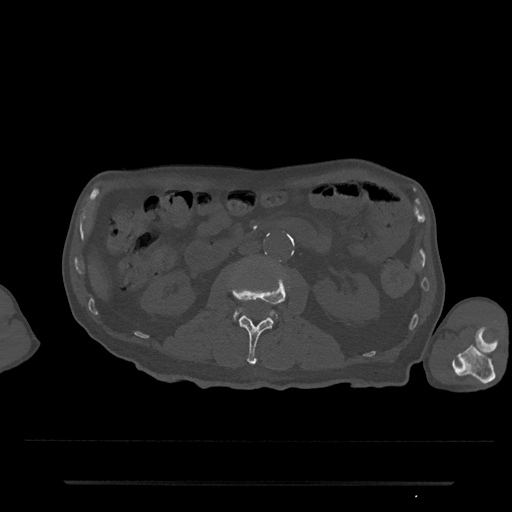
CT including the spine, one axial slice. Slice 37 of 797 in the series (ordered by position). Reconstruction kernel Br40s/3. 120 kVp. Bone window (W 1800 / L 400 HU). 512 × 512 image matrix. Male patient, age 74 years. Case-level facts recorded for this patient, not image findings: primary cancer: prostate.
Outlined on this slice (semi-automatic segmentation, software-assisted and operator-edited):
- L2 vertebra: bounding box (x1, y1, x2, y2) in pixels: (231, 277, 291, 365)
- L3 vertebra: (233, 307, 278, 321)